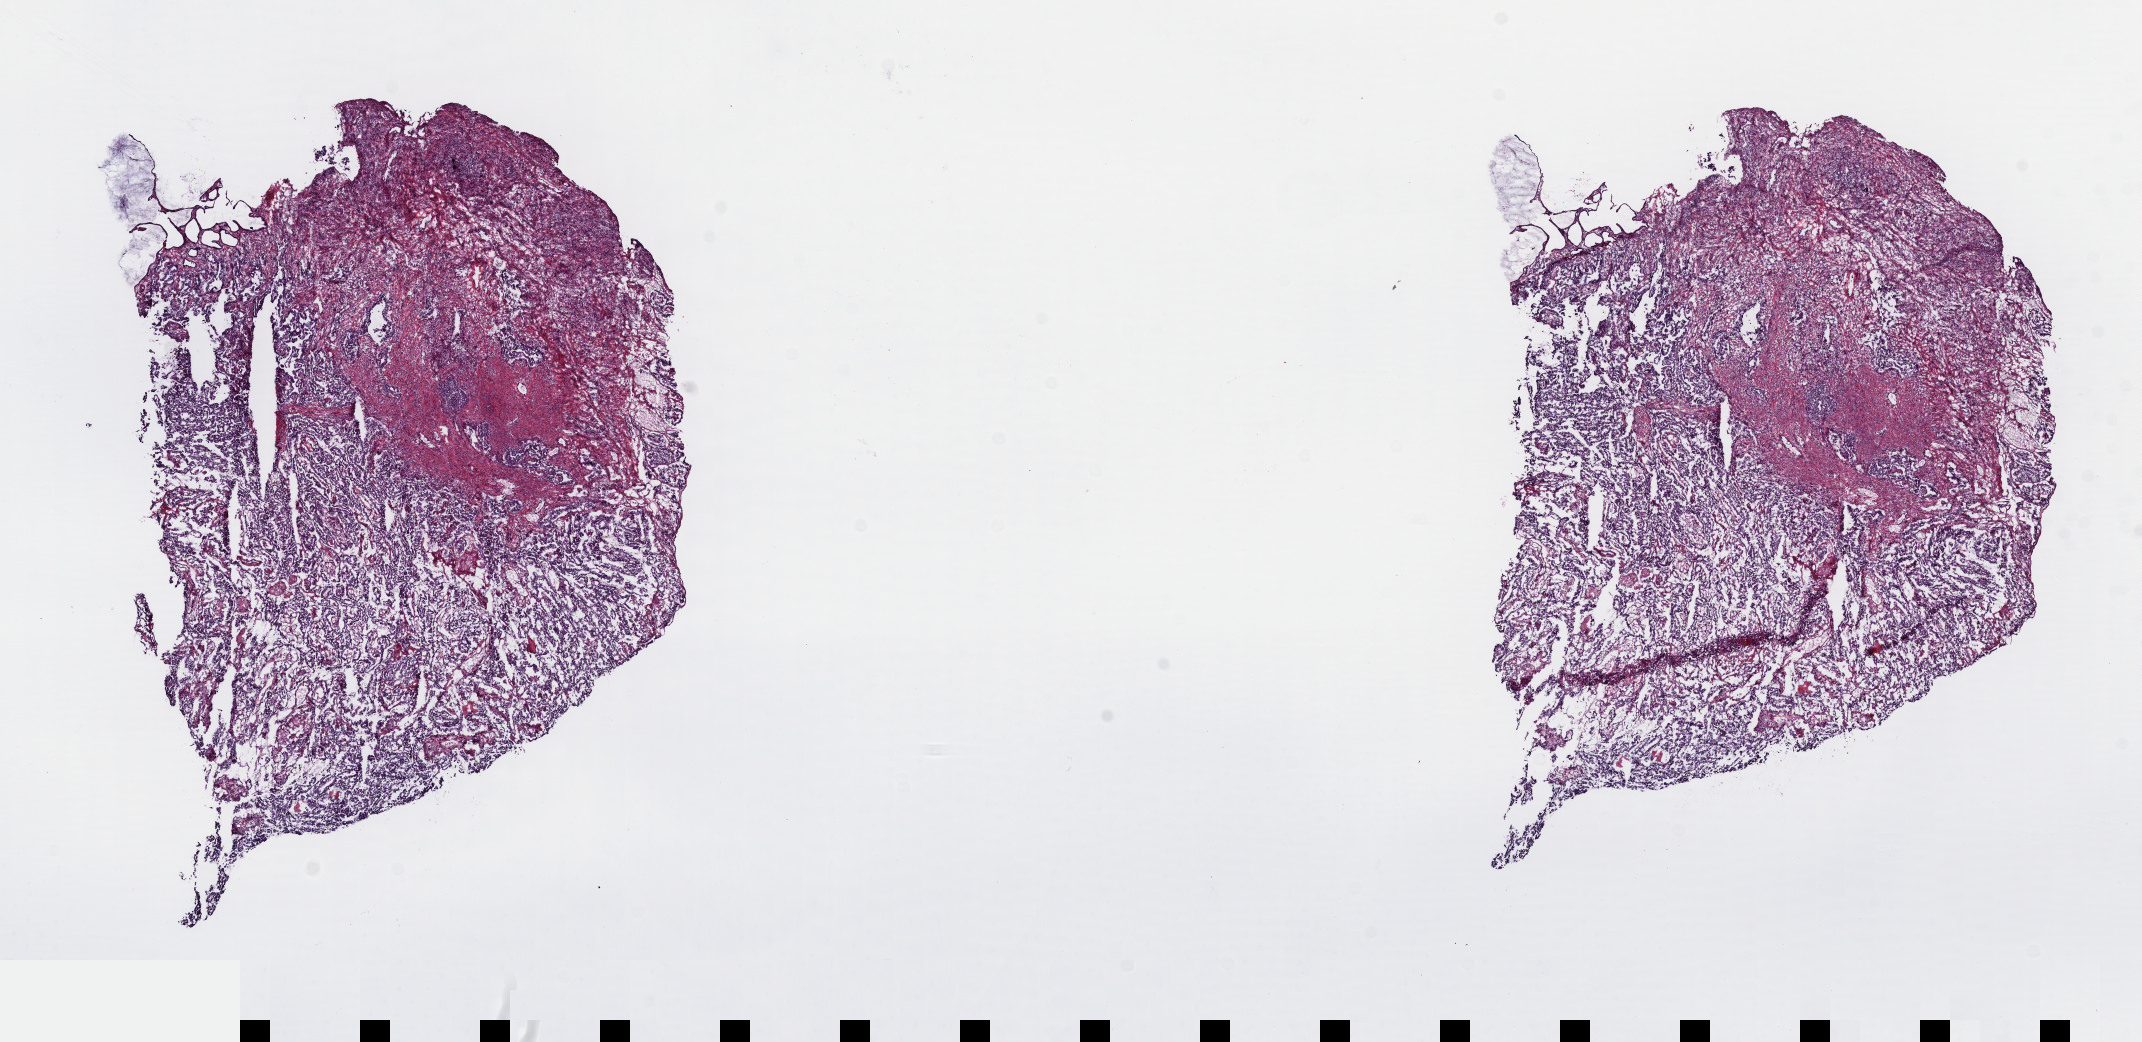
Hematoxylin and eosin (H&E) stained whole-slide image, shown as a low-resolution overview of the whole scanned area (about 16.9 x 8.2 mm, acquisition: 40x scan), frozen section, cervix, primary tumour sample. Patient: female, age at initial diagnosis 49 years. Histologic grade: G2 (moderately differentiated). Slide review estimates, as recorded: tumour cells 75%, tumour nuclei 75%, normal cells 0%, stromal cells 15%, necrosis 10%. Infiltration values recorded for this section: lymphocyte infiltration 20%, monocyte infiltration 20%, neutrophil infiltration 40%.
* FIGO stage: IB2
* lymph nodes positive (case pathology): 0 of 26 examined
* histologic diagnosis: Adenocarcinoma, endocervical type (endocervix)